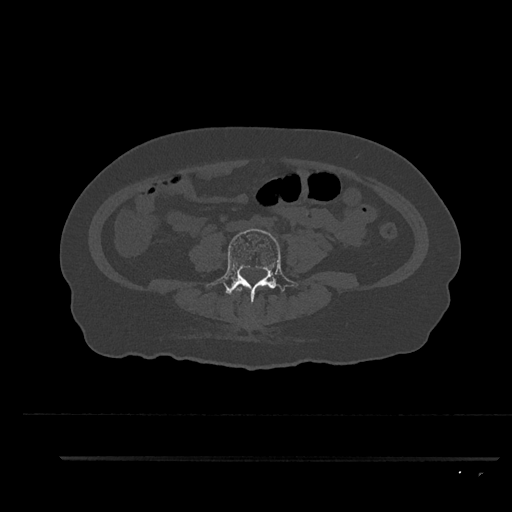
CT including the spine, one axial slice. Reconstruction kernel Br40s/3. Bone window (W 1800 / L 400 HU). 0.5 mm slice thickness. 512 × 512 image matrix. Female patient, age 44 years. Case-level facts recorded for this patient, not image findings: primary cancer: renal.
Outlined on this slice (semi-automatic segmentation, software-assisted and operator-edited):
- L3 vertebra: bounding box (x1, y1, x2, y2) in pixels: (235, 286, 242, 292)
- L4 vertebra: (207, 229, 299, 304)